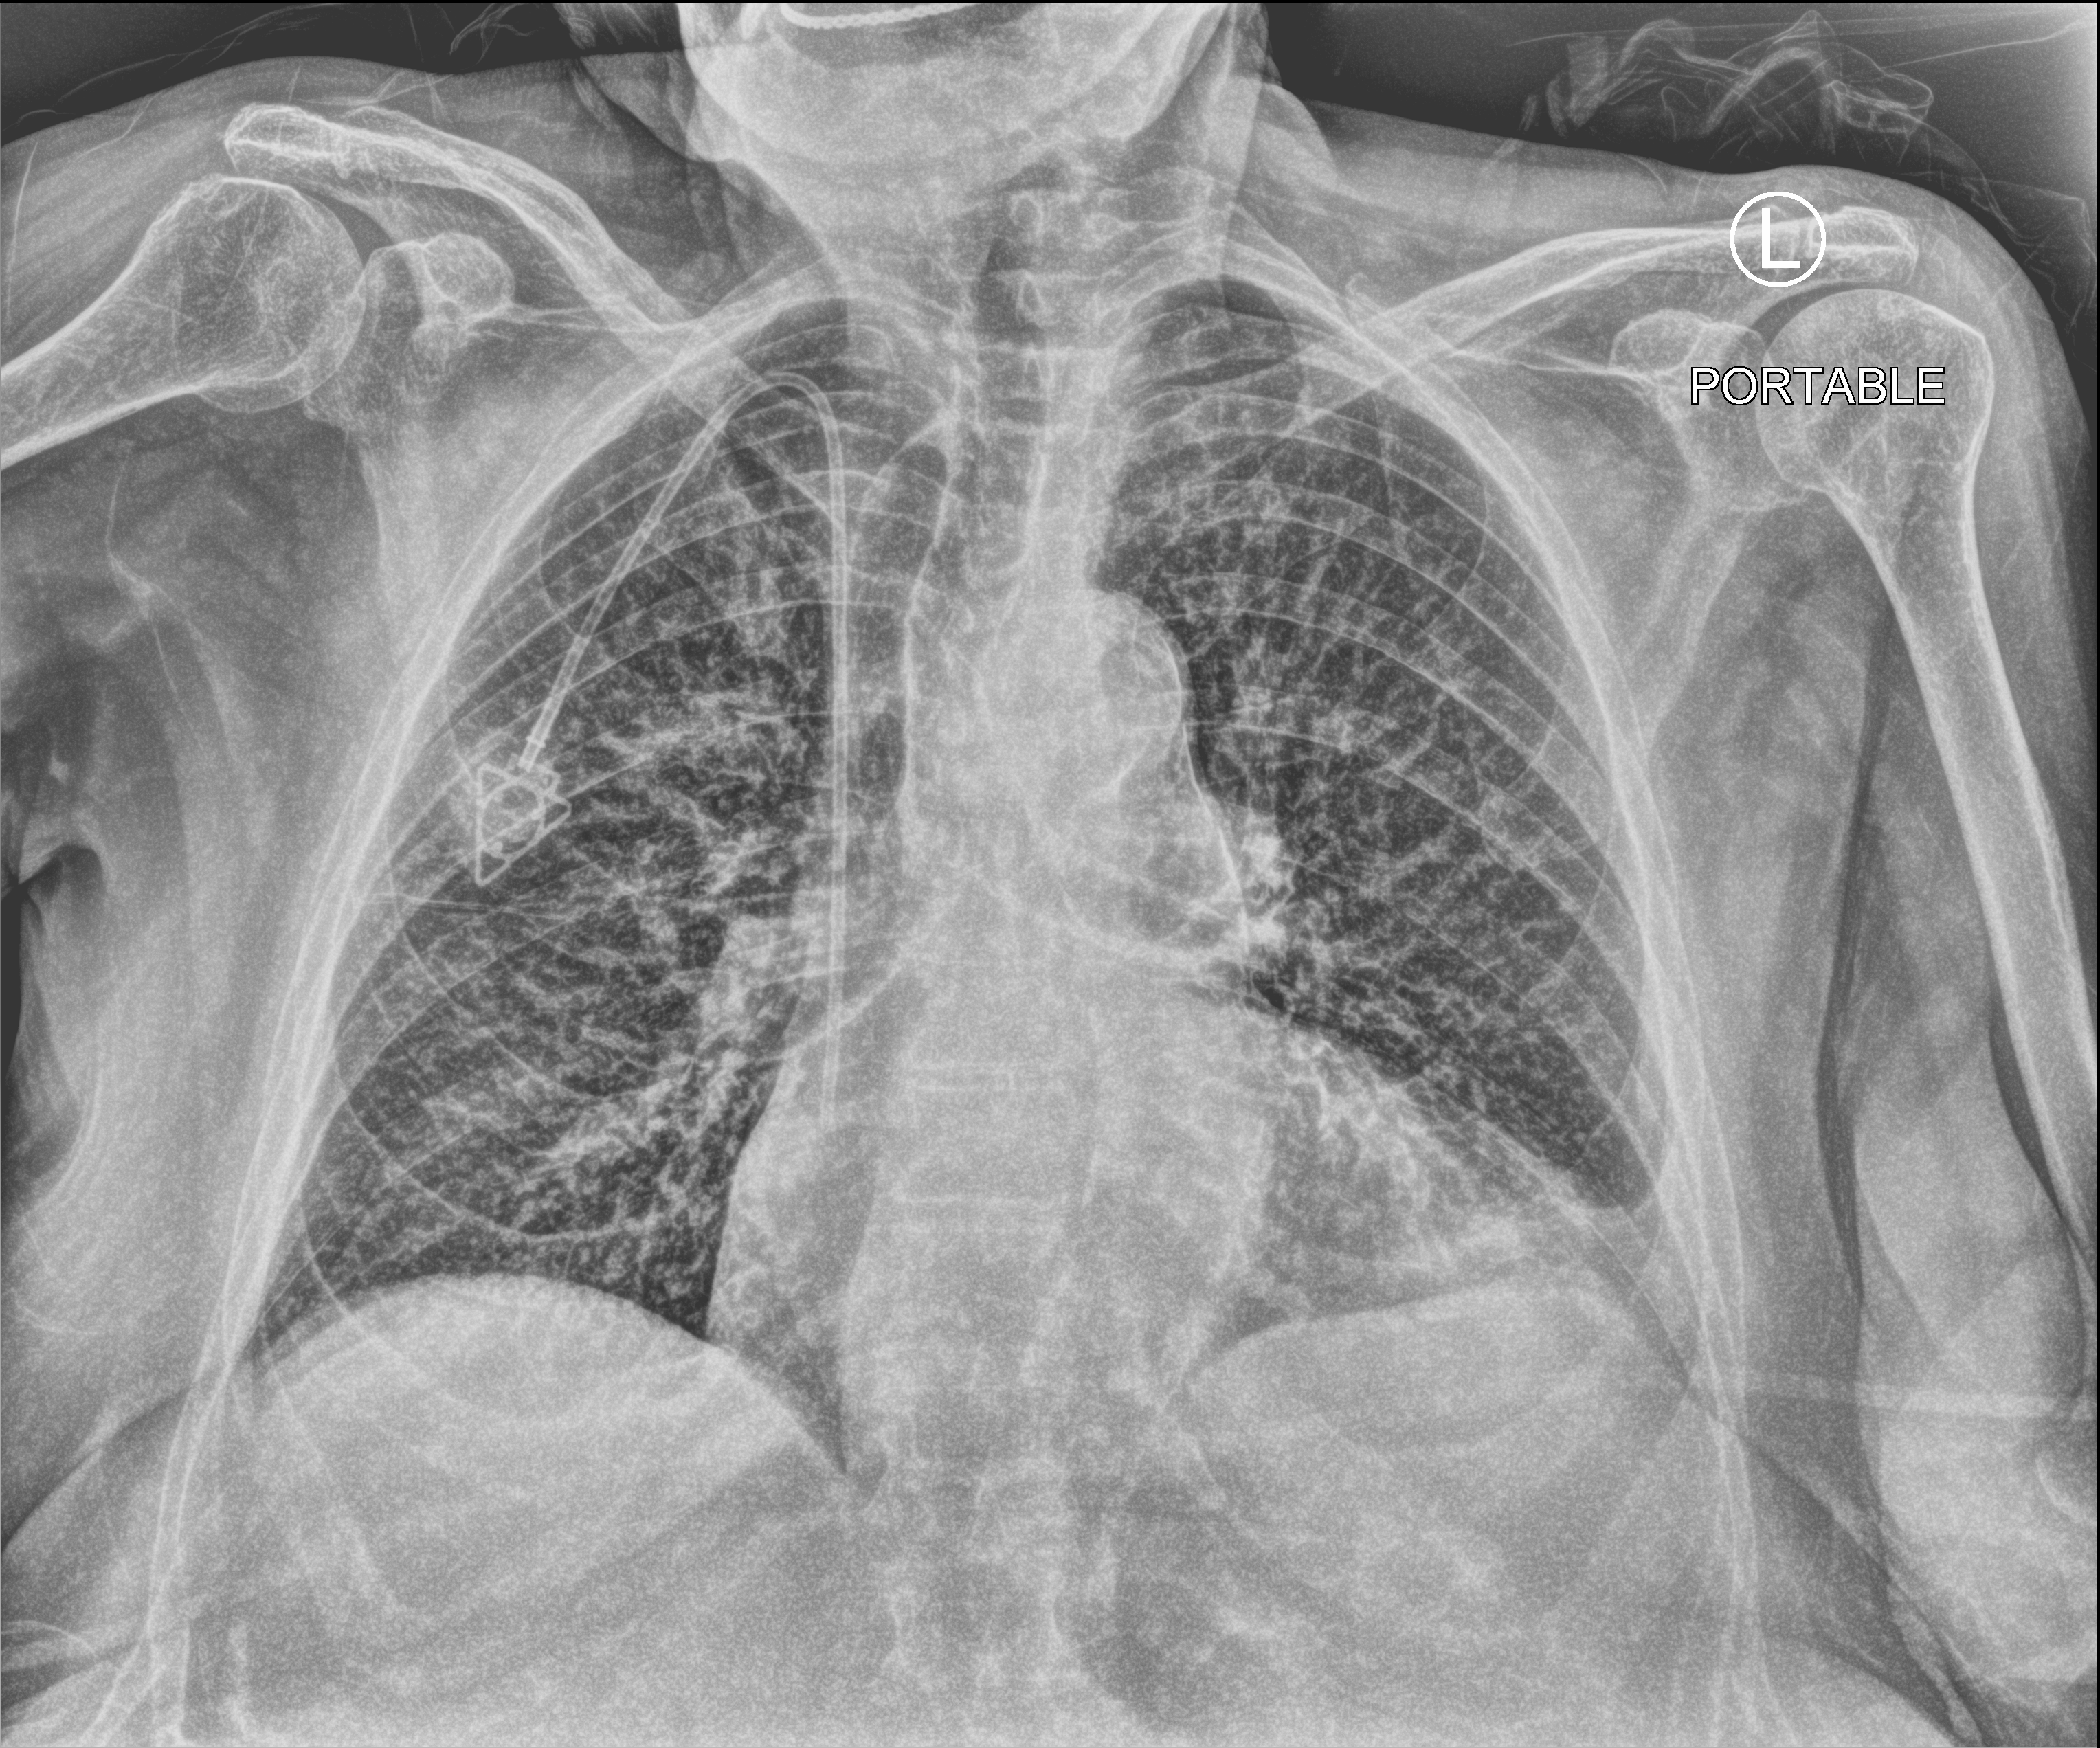
Chest X-ray (portable); anteroposterior (AP) projection. Patient hospitalised with COVID-19; female, aged 75–90 years.
Hospital-stay facts (about this admission, not read from this image; timing relative to this image not recorded):
- admitted to intensive care during this hospital stay: no
- mechanically ventilated during this hospital stay: no